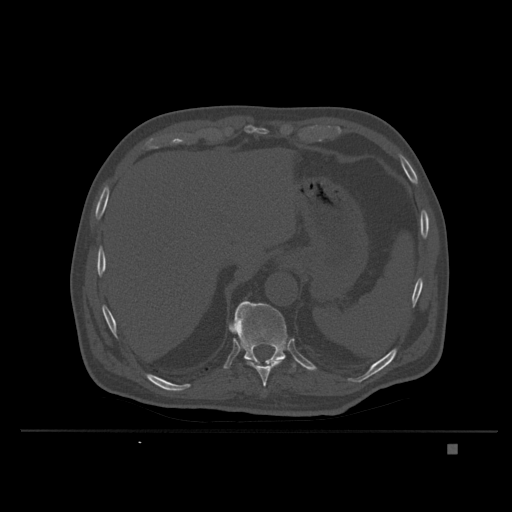
CT including the spine, one axial slice; slice 186 of 435 in the series (ordered by position); bone window (W 1800 / L 400 HU); 1.5 mm slice thickness; 512 × 512 image matrix, field of view 434 × 434 mm. Male patient, age 73 years. From the clinical record (not read from this slice): primary cancer: skin.
Outlined on this slice (semi-automatic segmentation, software-assisted and operator-edited):
- T10 vertebra: bounding box (x1, y1, x2, y2) in pixels: (244, 358, 285, 387)
- T11 vertebra: (229, 301, 298, 372)
- T9 vertebra: (264, 390, 267, 392)